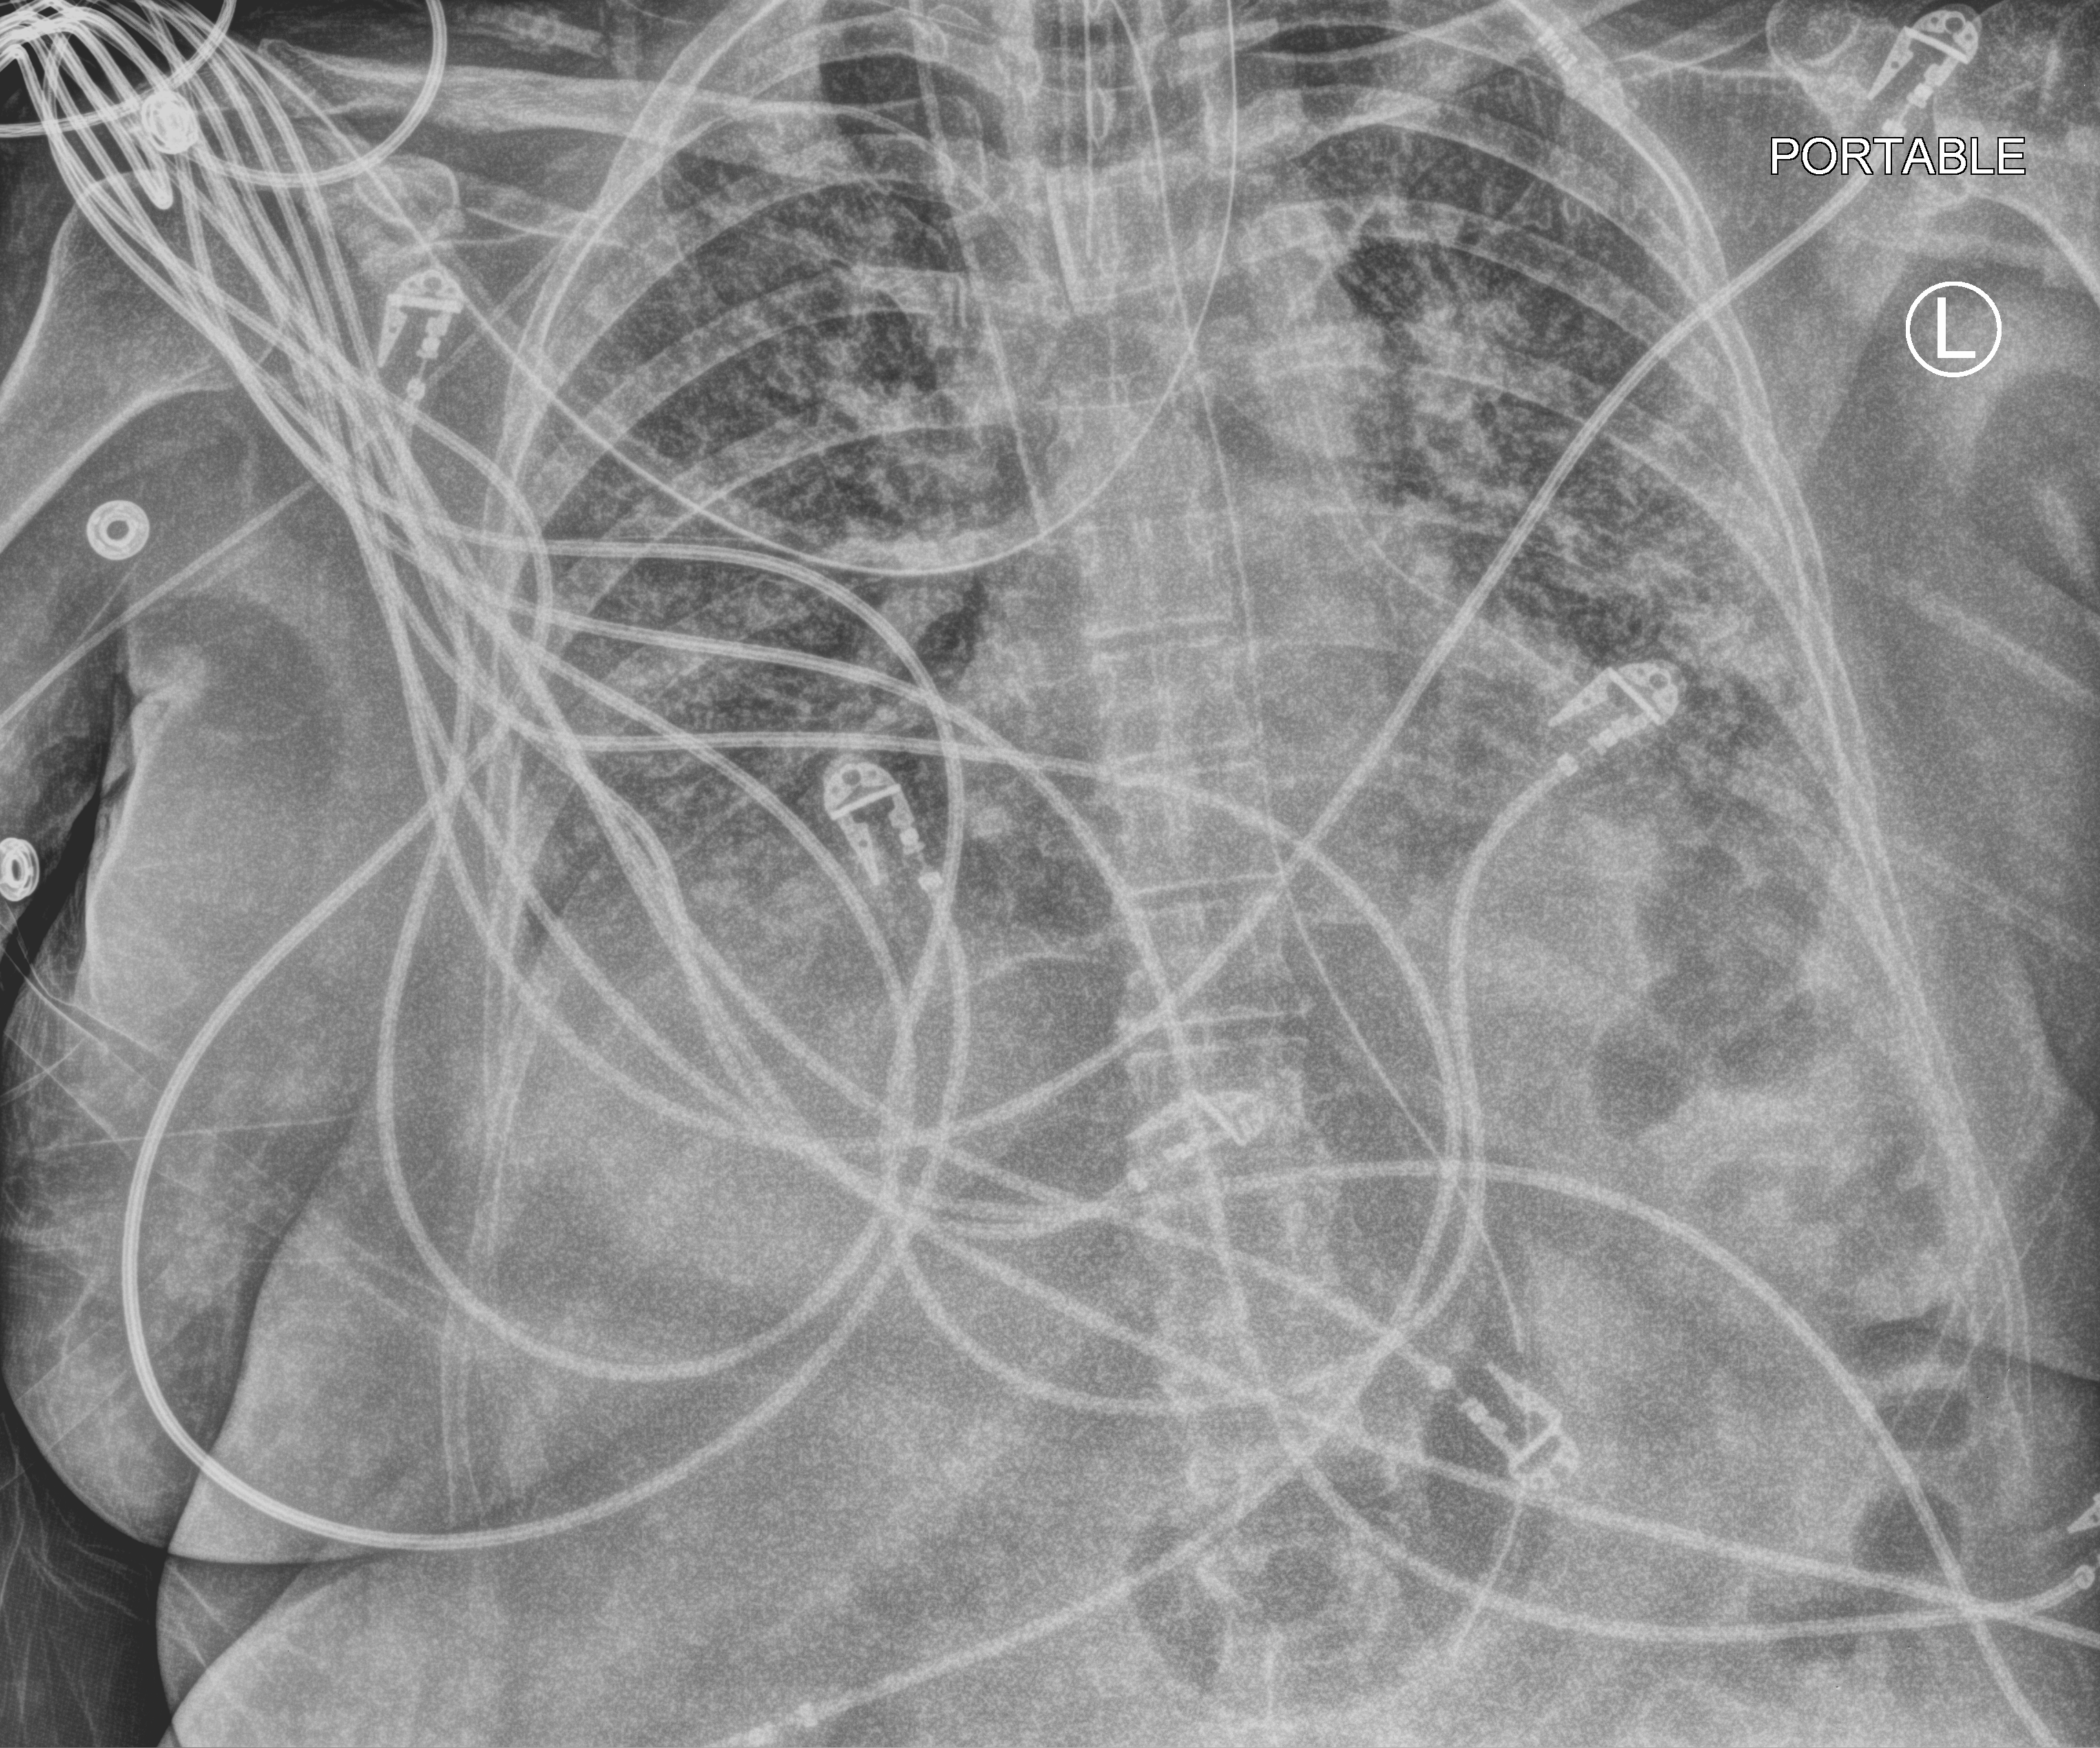
Chest X-ray (portable); anteroposterior (AP) projection. Female patient hospitalised with COVID-19, age 60–74 years.
Admission-level facts for this patient (not findings on this image; timing relative to this image not recorded): mechanically ventilated during this hospital stay: yes; other chronic lung disease (admission record): no.